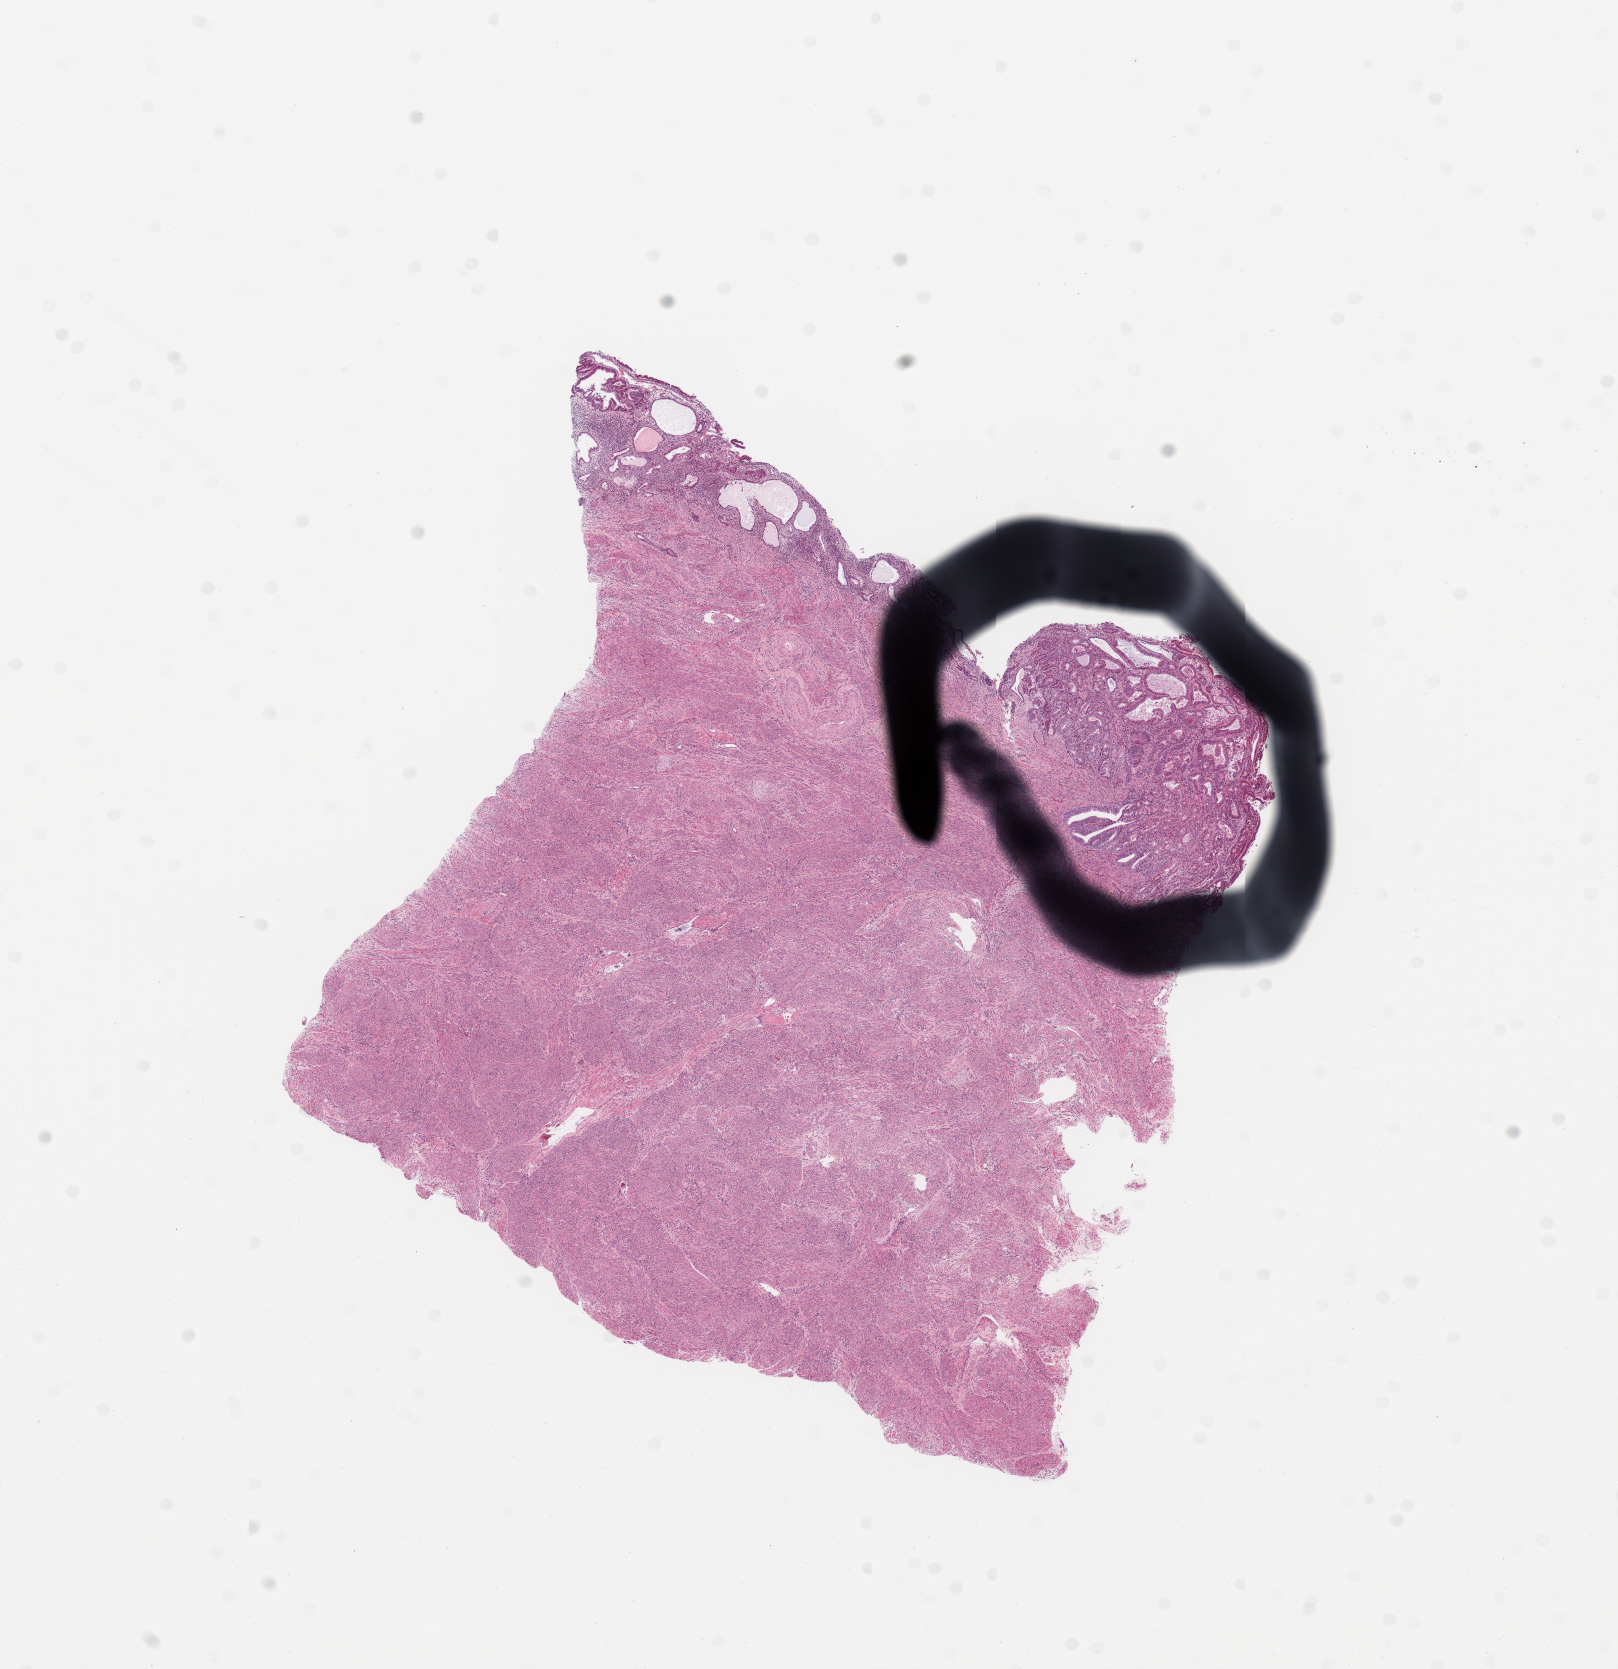
Digitized H&E-stained tissue section (whole slide) — low-resolution overview of the scanned area, about 12.8 x 13.2 mm (acquisition: 20x scan), uterus, normal (non-tumour) tissue. Female, 56 y/o.
This section: normal (non-tumour) tissue from the same patient. Patient diagnosis: Endometrioid adenocarcinoma, NOS.